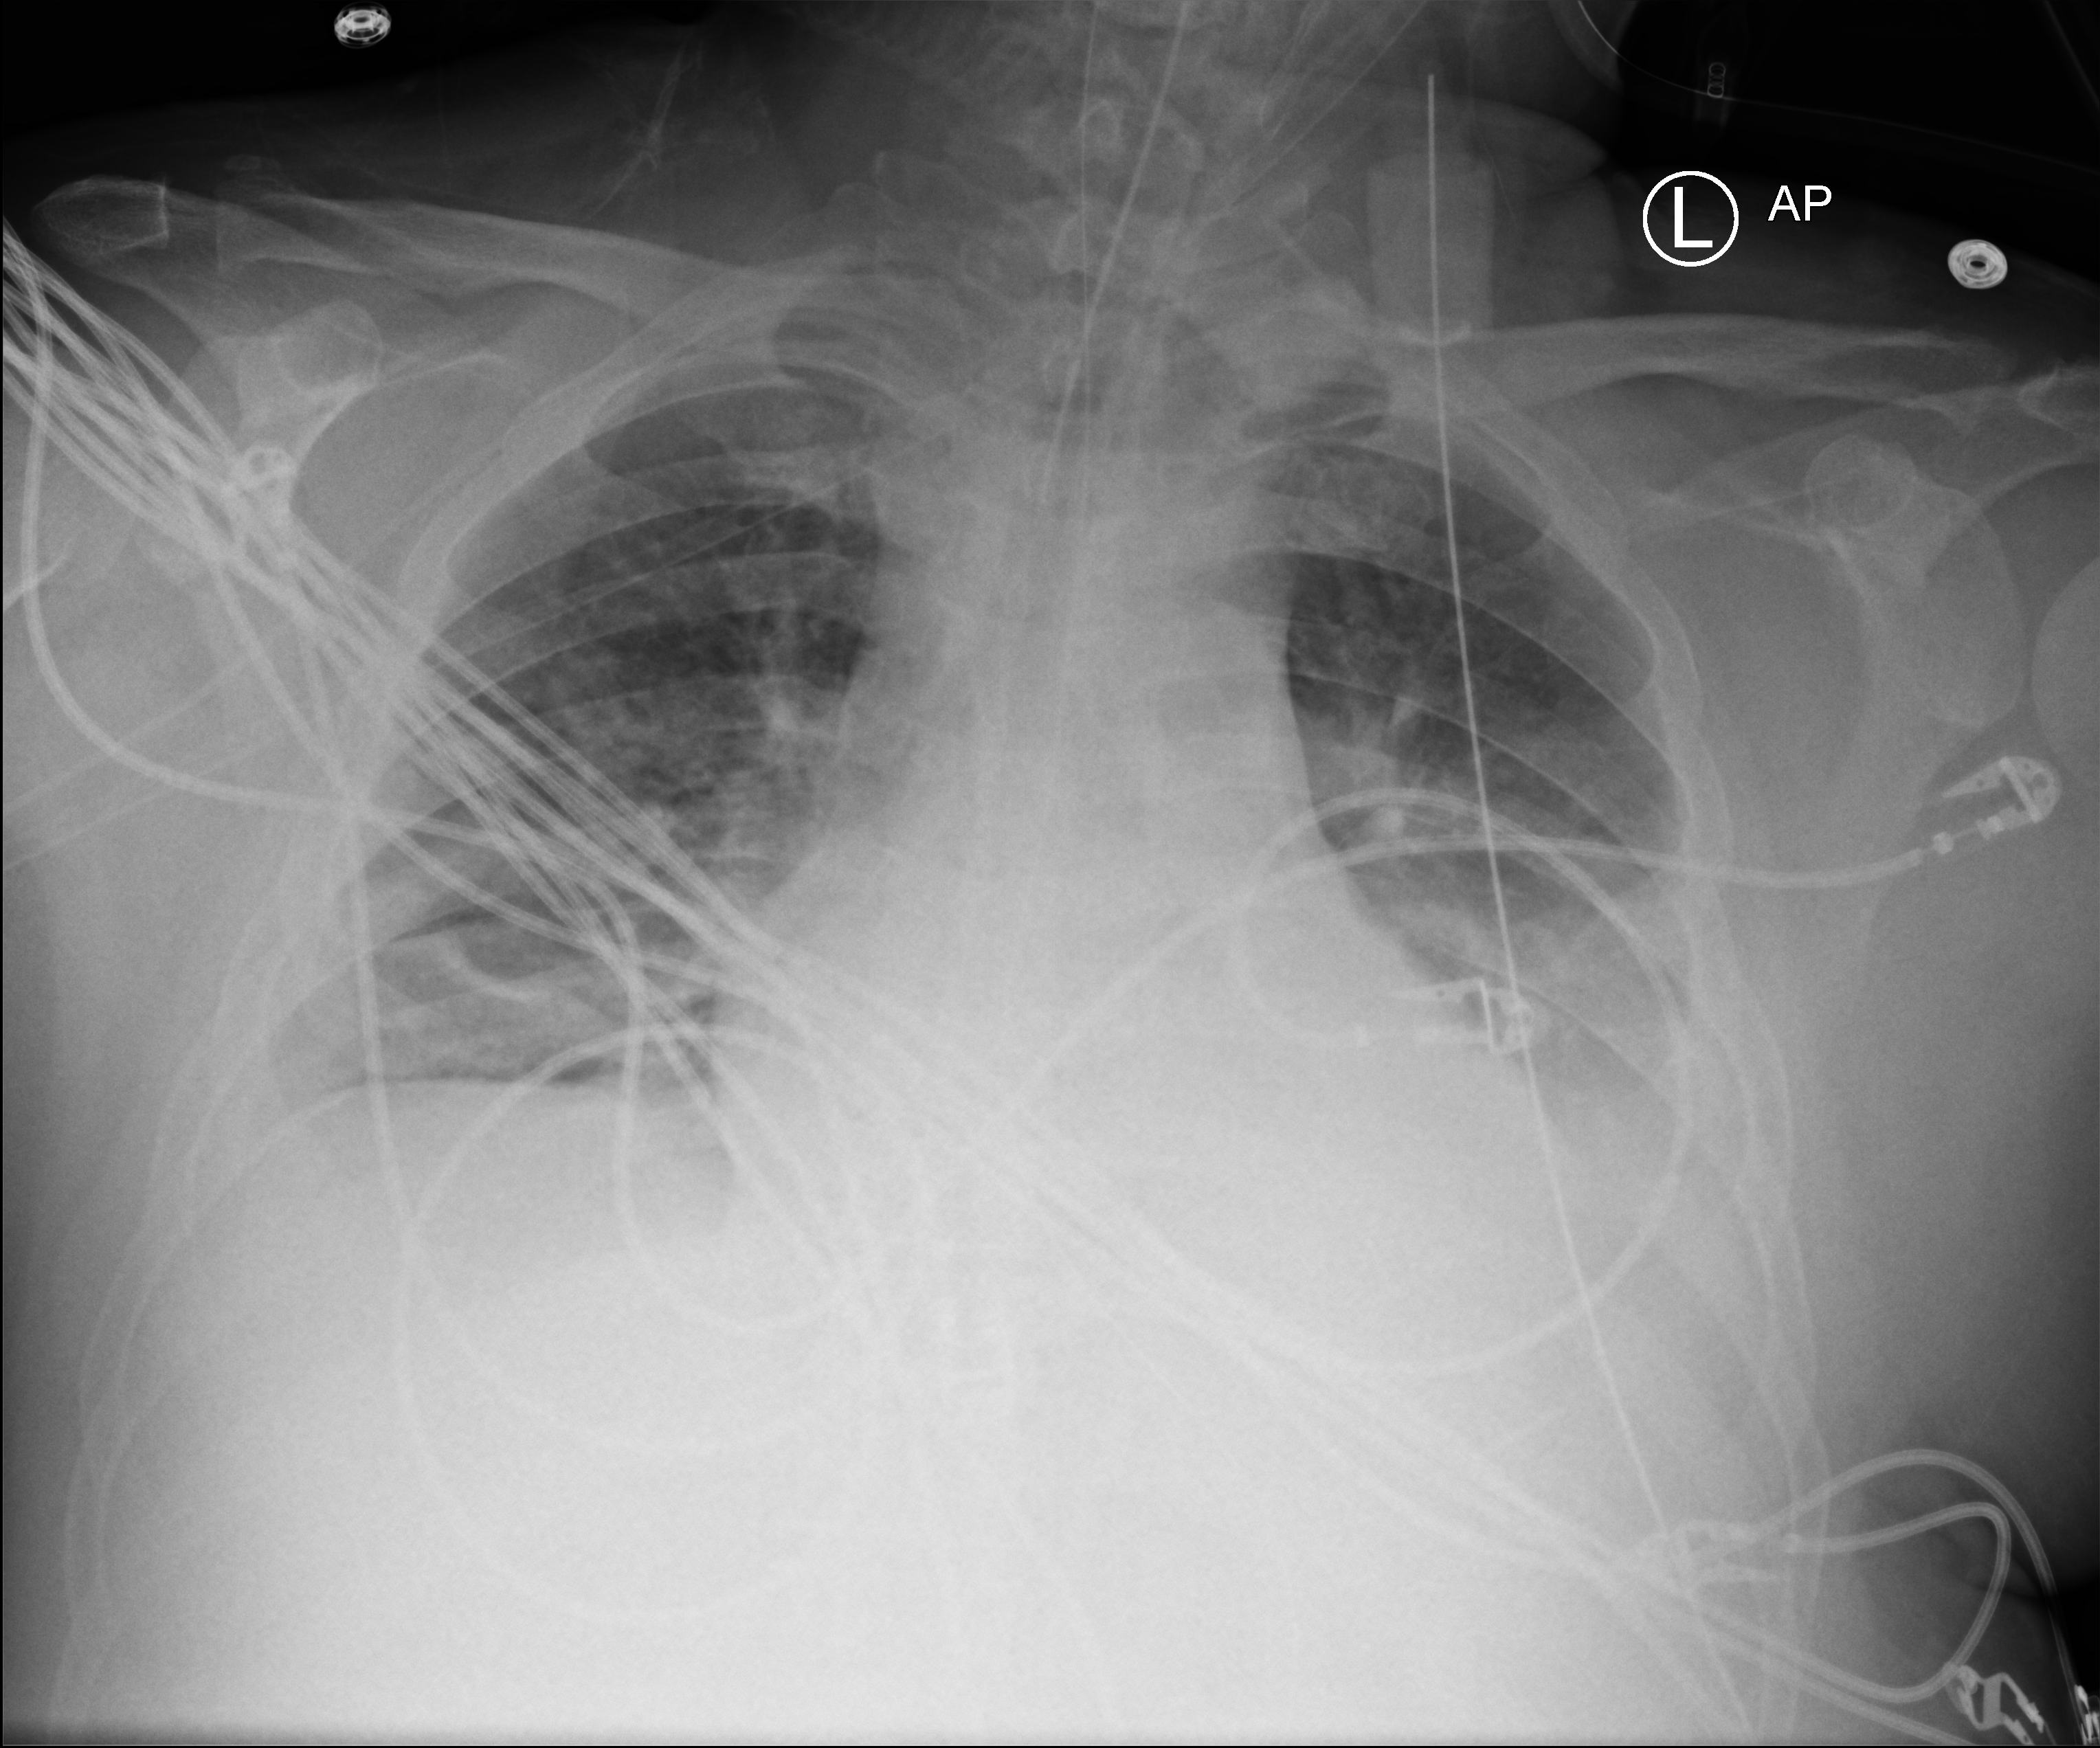
Bedside chest radiograph (computed radiography), anteroposterior (AP) projection. Male patient hospitalised with COVID-19, age 18–59 years.
From the hospital-stay record, not from the radiograph (when in the stay this image was taken is not recorded): admitted to intensive care during this hospital stay: yes.